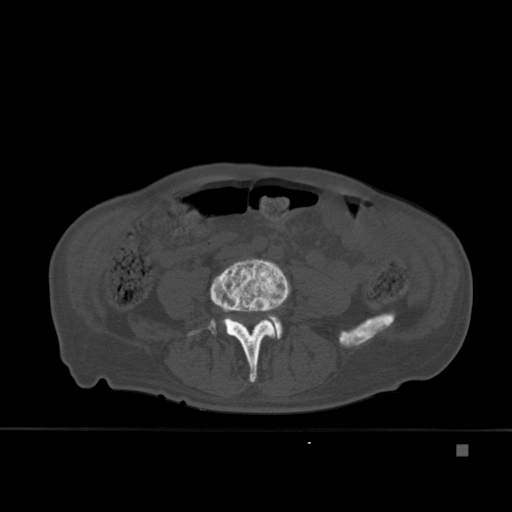
CT including the spine, one axial slice; slice 119 of 451 in the series (ordered by position); bone window (W 1800 / L 400 HU); 1.5 mm slice thickness; 512 × 512 image matrix, field of view 378 × 378 mm. Patient: male, 75 years. Case-level facts recorded for this patient, not image findings: primary cancer: prostate.
Outlined on this slice (semi-automatic segmentation, software-assisted and operator-edited):
- L4 vertebra: box from (x=188, y=259) to (x=291, y=383) px
- L5 vertebra: (x=267, y=314)–(x=283, y=339)